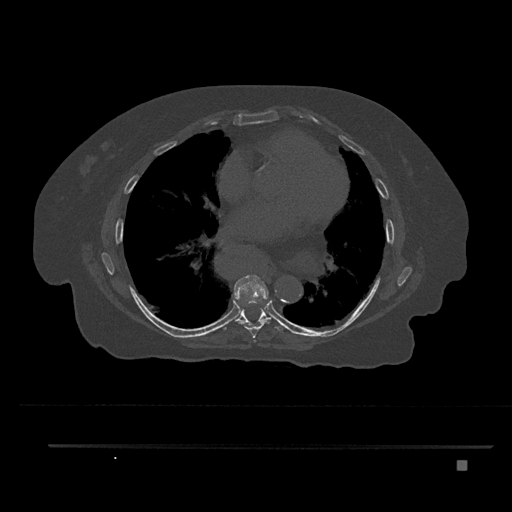
CT including the spine, one axial slice; bone window (W 1800 / L 400 HU); 0.5 mm slice thickness; 512 × 512 image matrix, field of view 437 × 437 mm. Patient: female, 76 years. From the clinical record (not read from this slice): primary cancer: lung.
Outlined on this slice (semi-automatic segmentation, software-assisted and operator-edited):
- T6 vertebra: bounding box (x1, y1, x2, y2) in pixels: (253, 340, 256, 343)
- T7 vertebra: (233, 275, 271, 339)
- T8 vertebra: (224, 306, 289, 331)